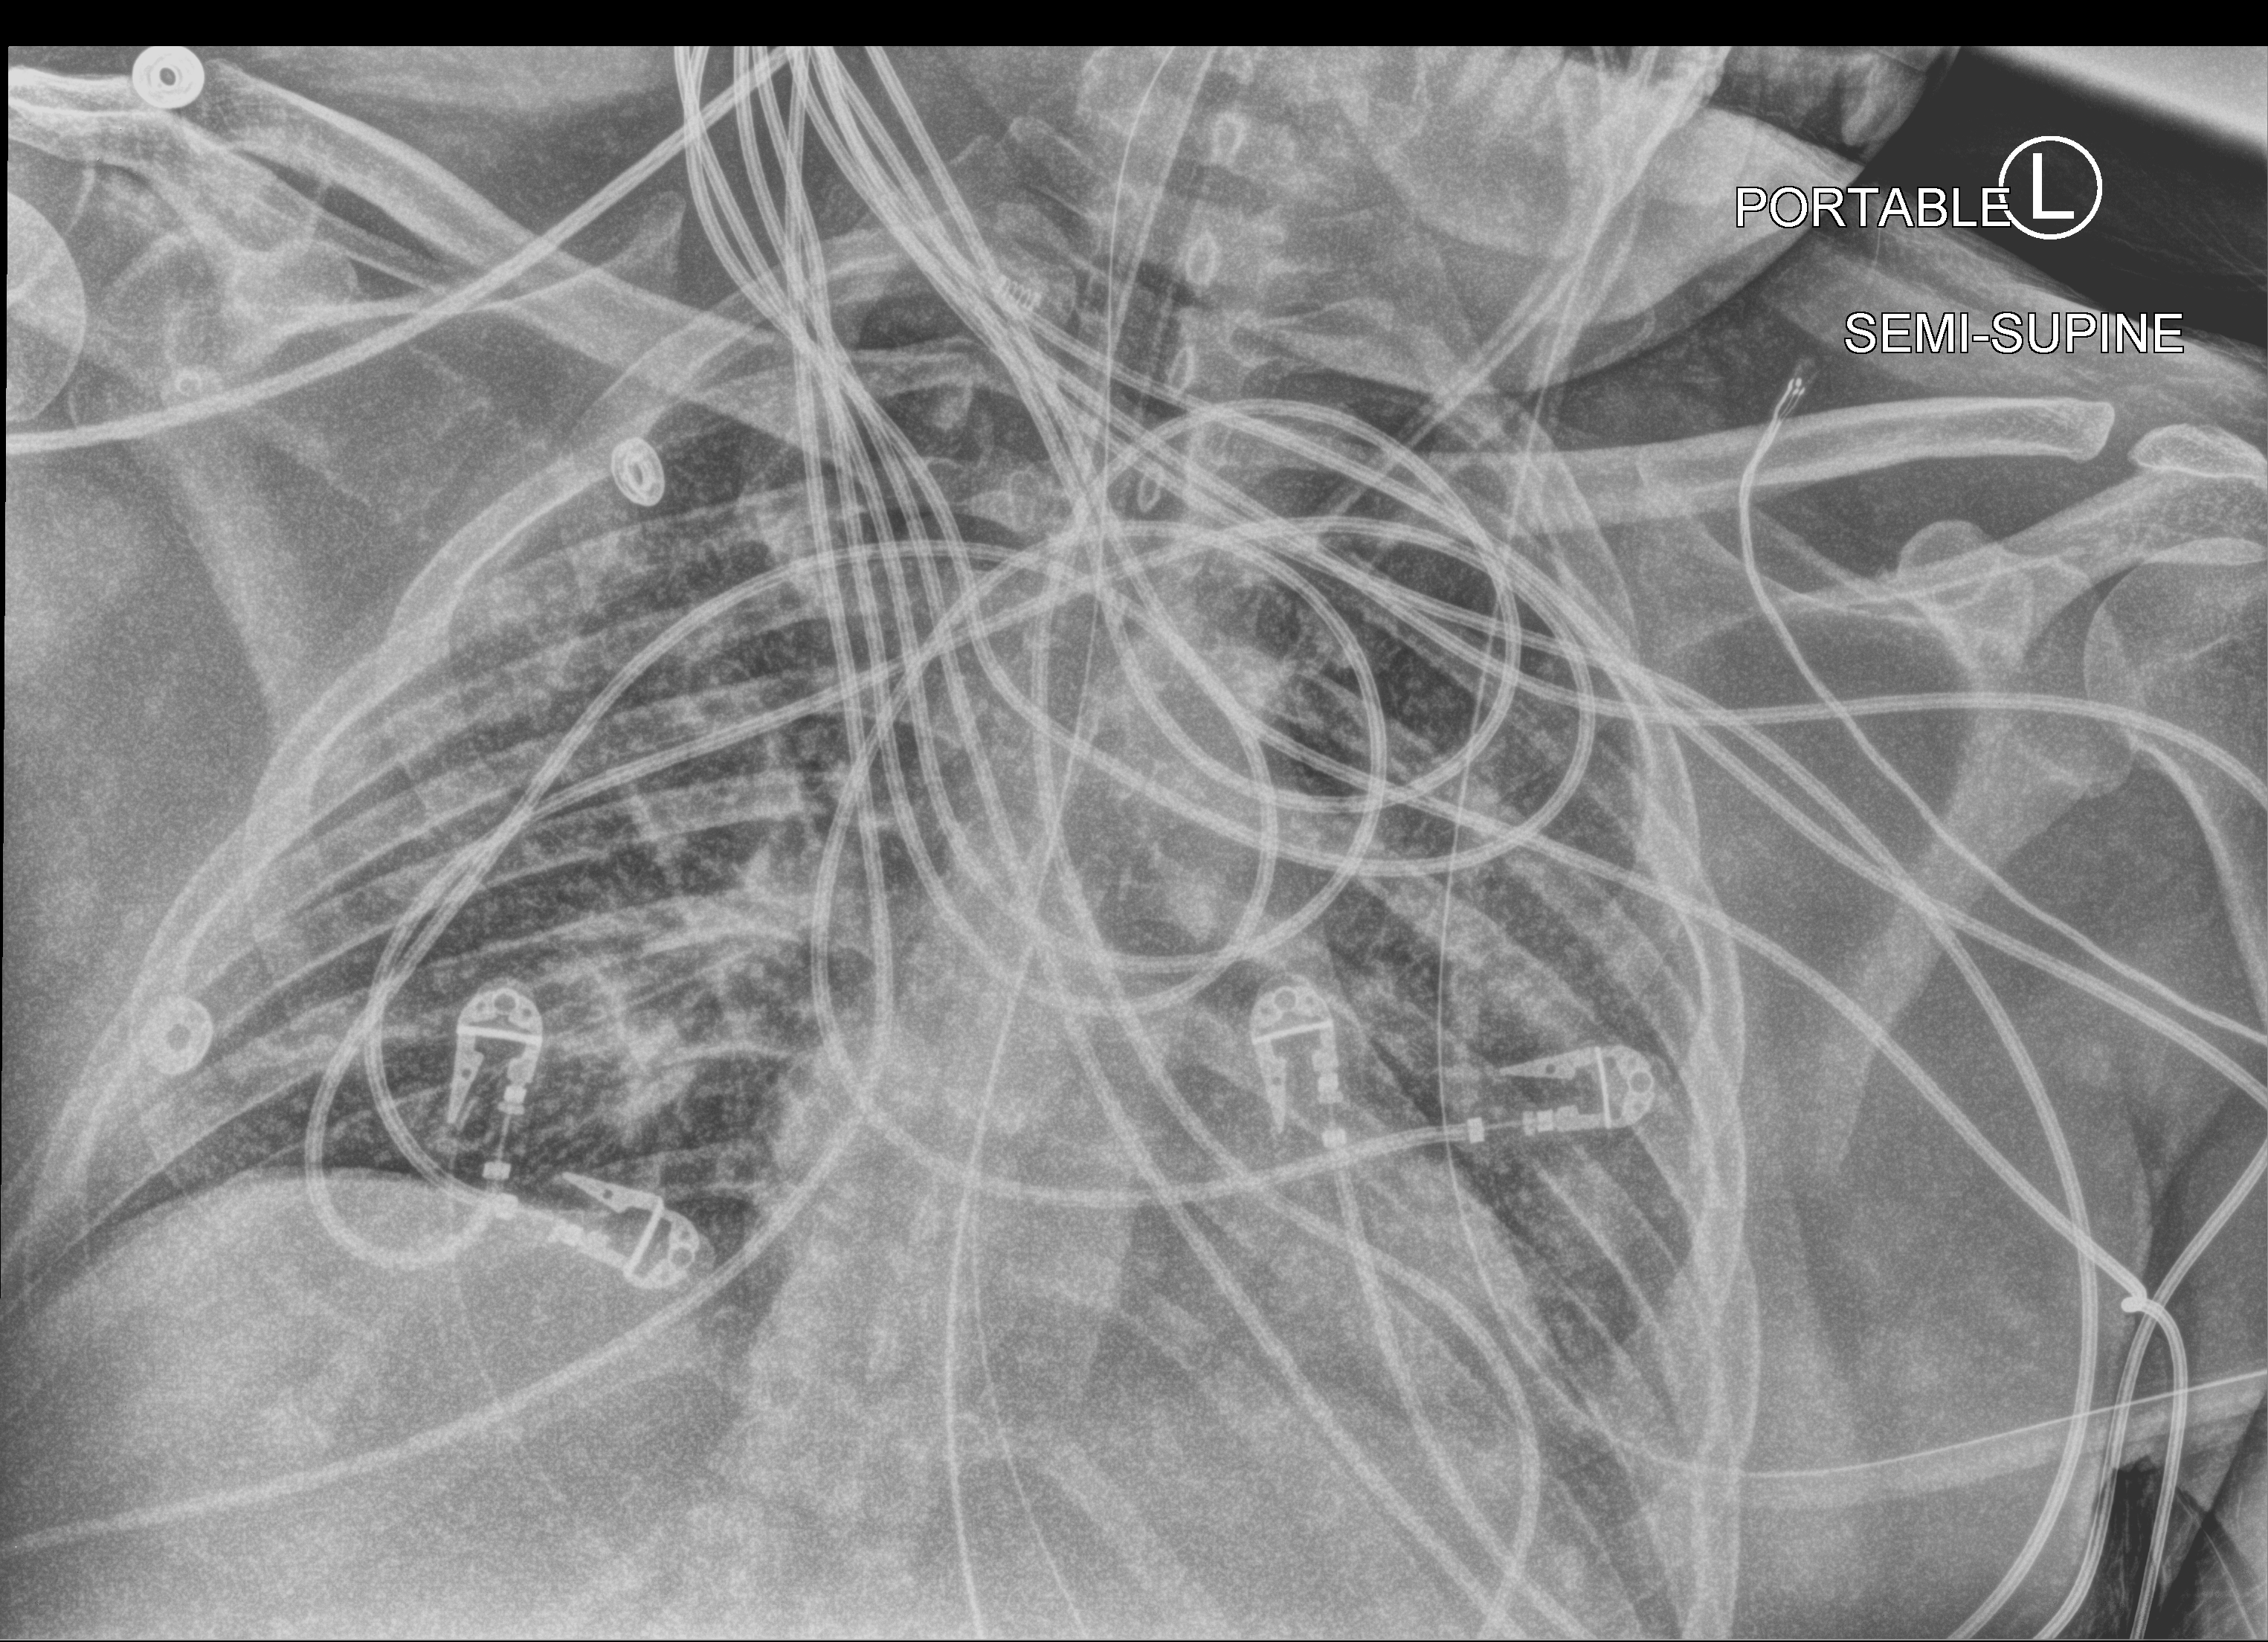
Chest X-ray (portable); anteroposterior (AP) projection. Patient hospitalised with COVID-19, aged 18–59 years.
Hospital-stay facts (about this admission, not read from this image; timing relative to this image not recorded): admitted to intensive care during this hospital stay: yes; mechanically ventilated during this hospital stay: yes; hypertension (admission record): yes.